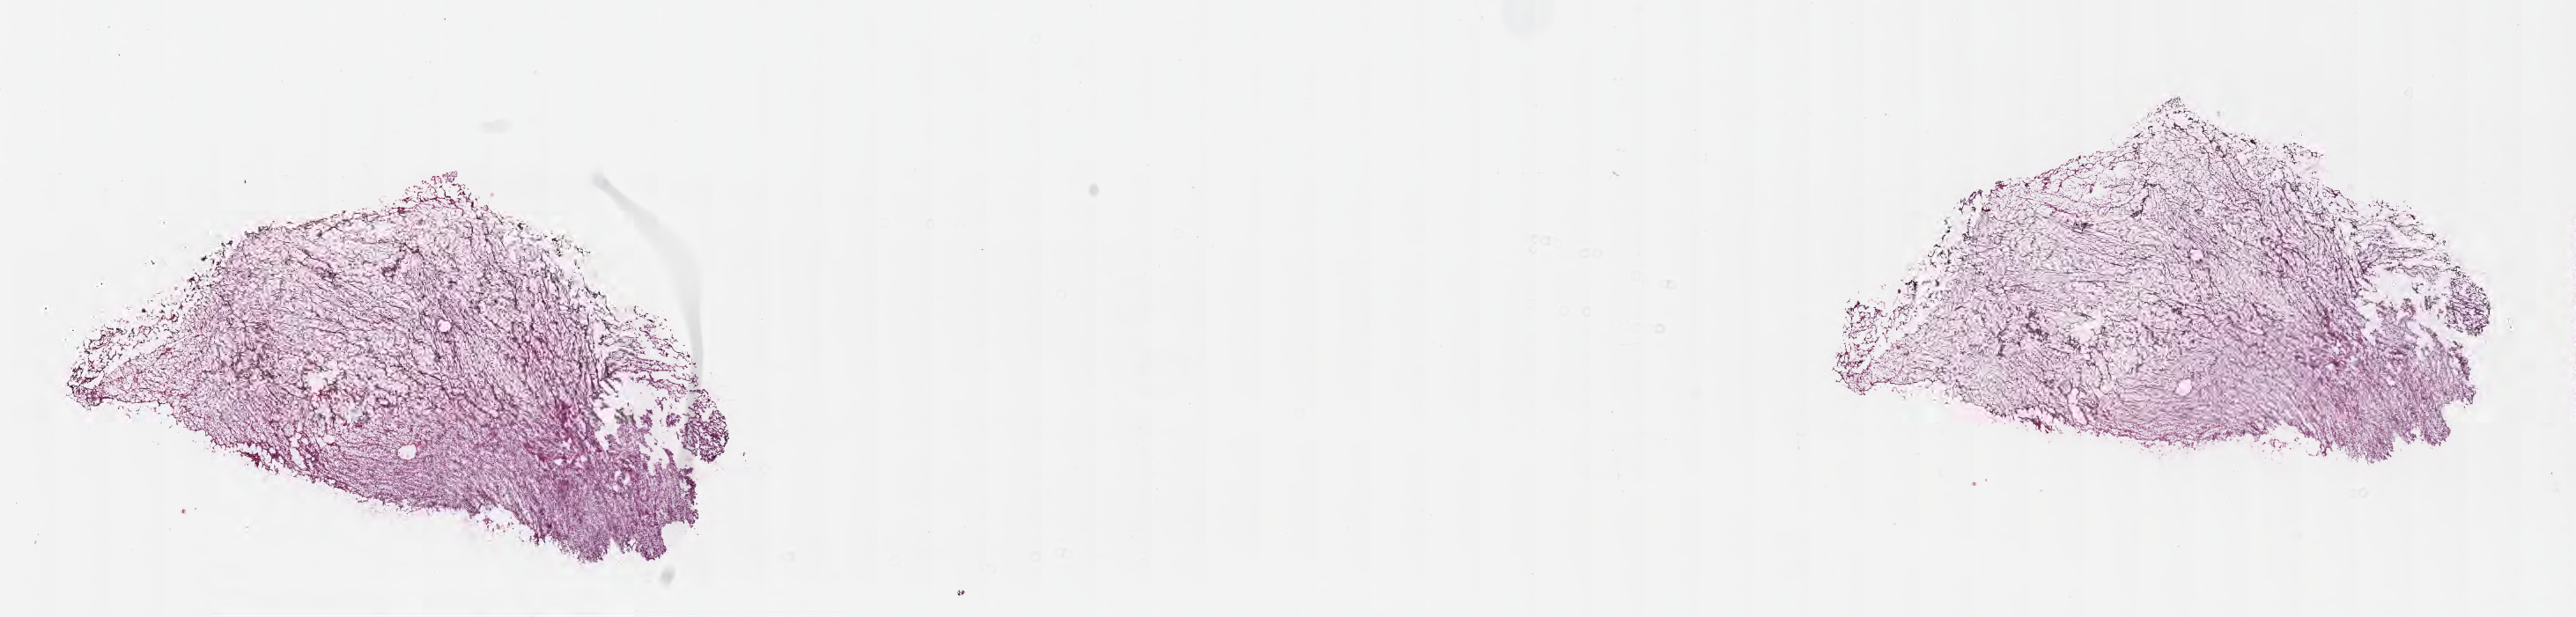
H&E whole-slide image — a low-resolution overview of the entire scanned area, about 23.6 x 5.7 mm; frozen section (tissue freezing medium); primary tumor; site: soft tissue. Female, age 25 years at initial diagnosis. Composition of this section per pathologist review: tumor cells 80%, tumor nuclei 90%, stromal cells 20%, necrosis 0%, normal cells 0%. Inflammatory infiltration, as recorded: lymphocyte infiltration 0%, monocyte infiltration 0%, neutrophil infiltration 0%.
Diagnosis: Spindle cell sarcoma. Section: top of the tissue portion.